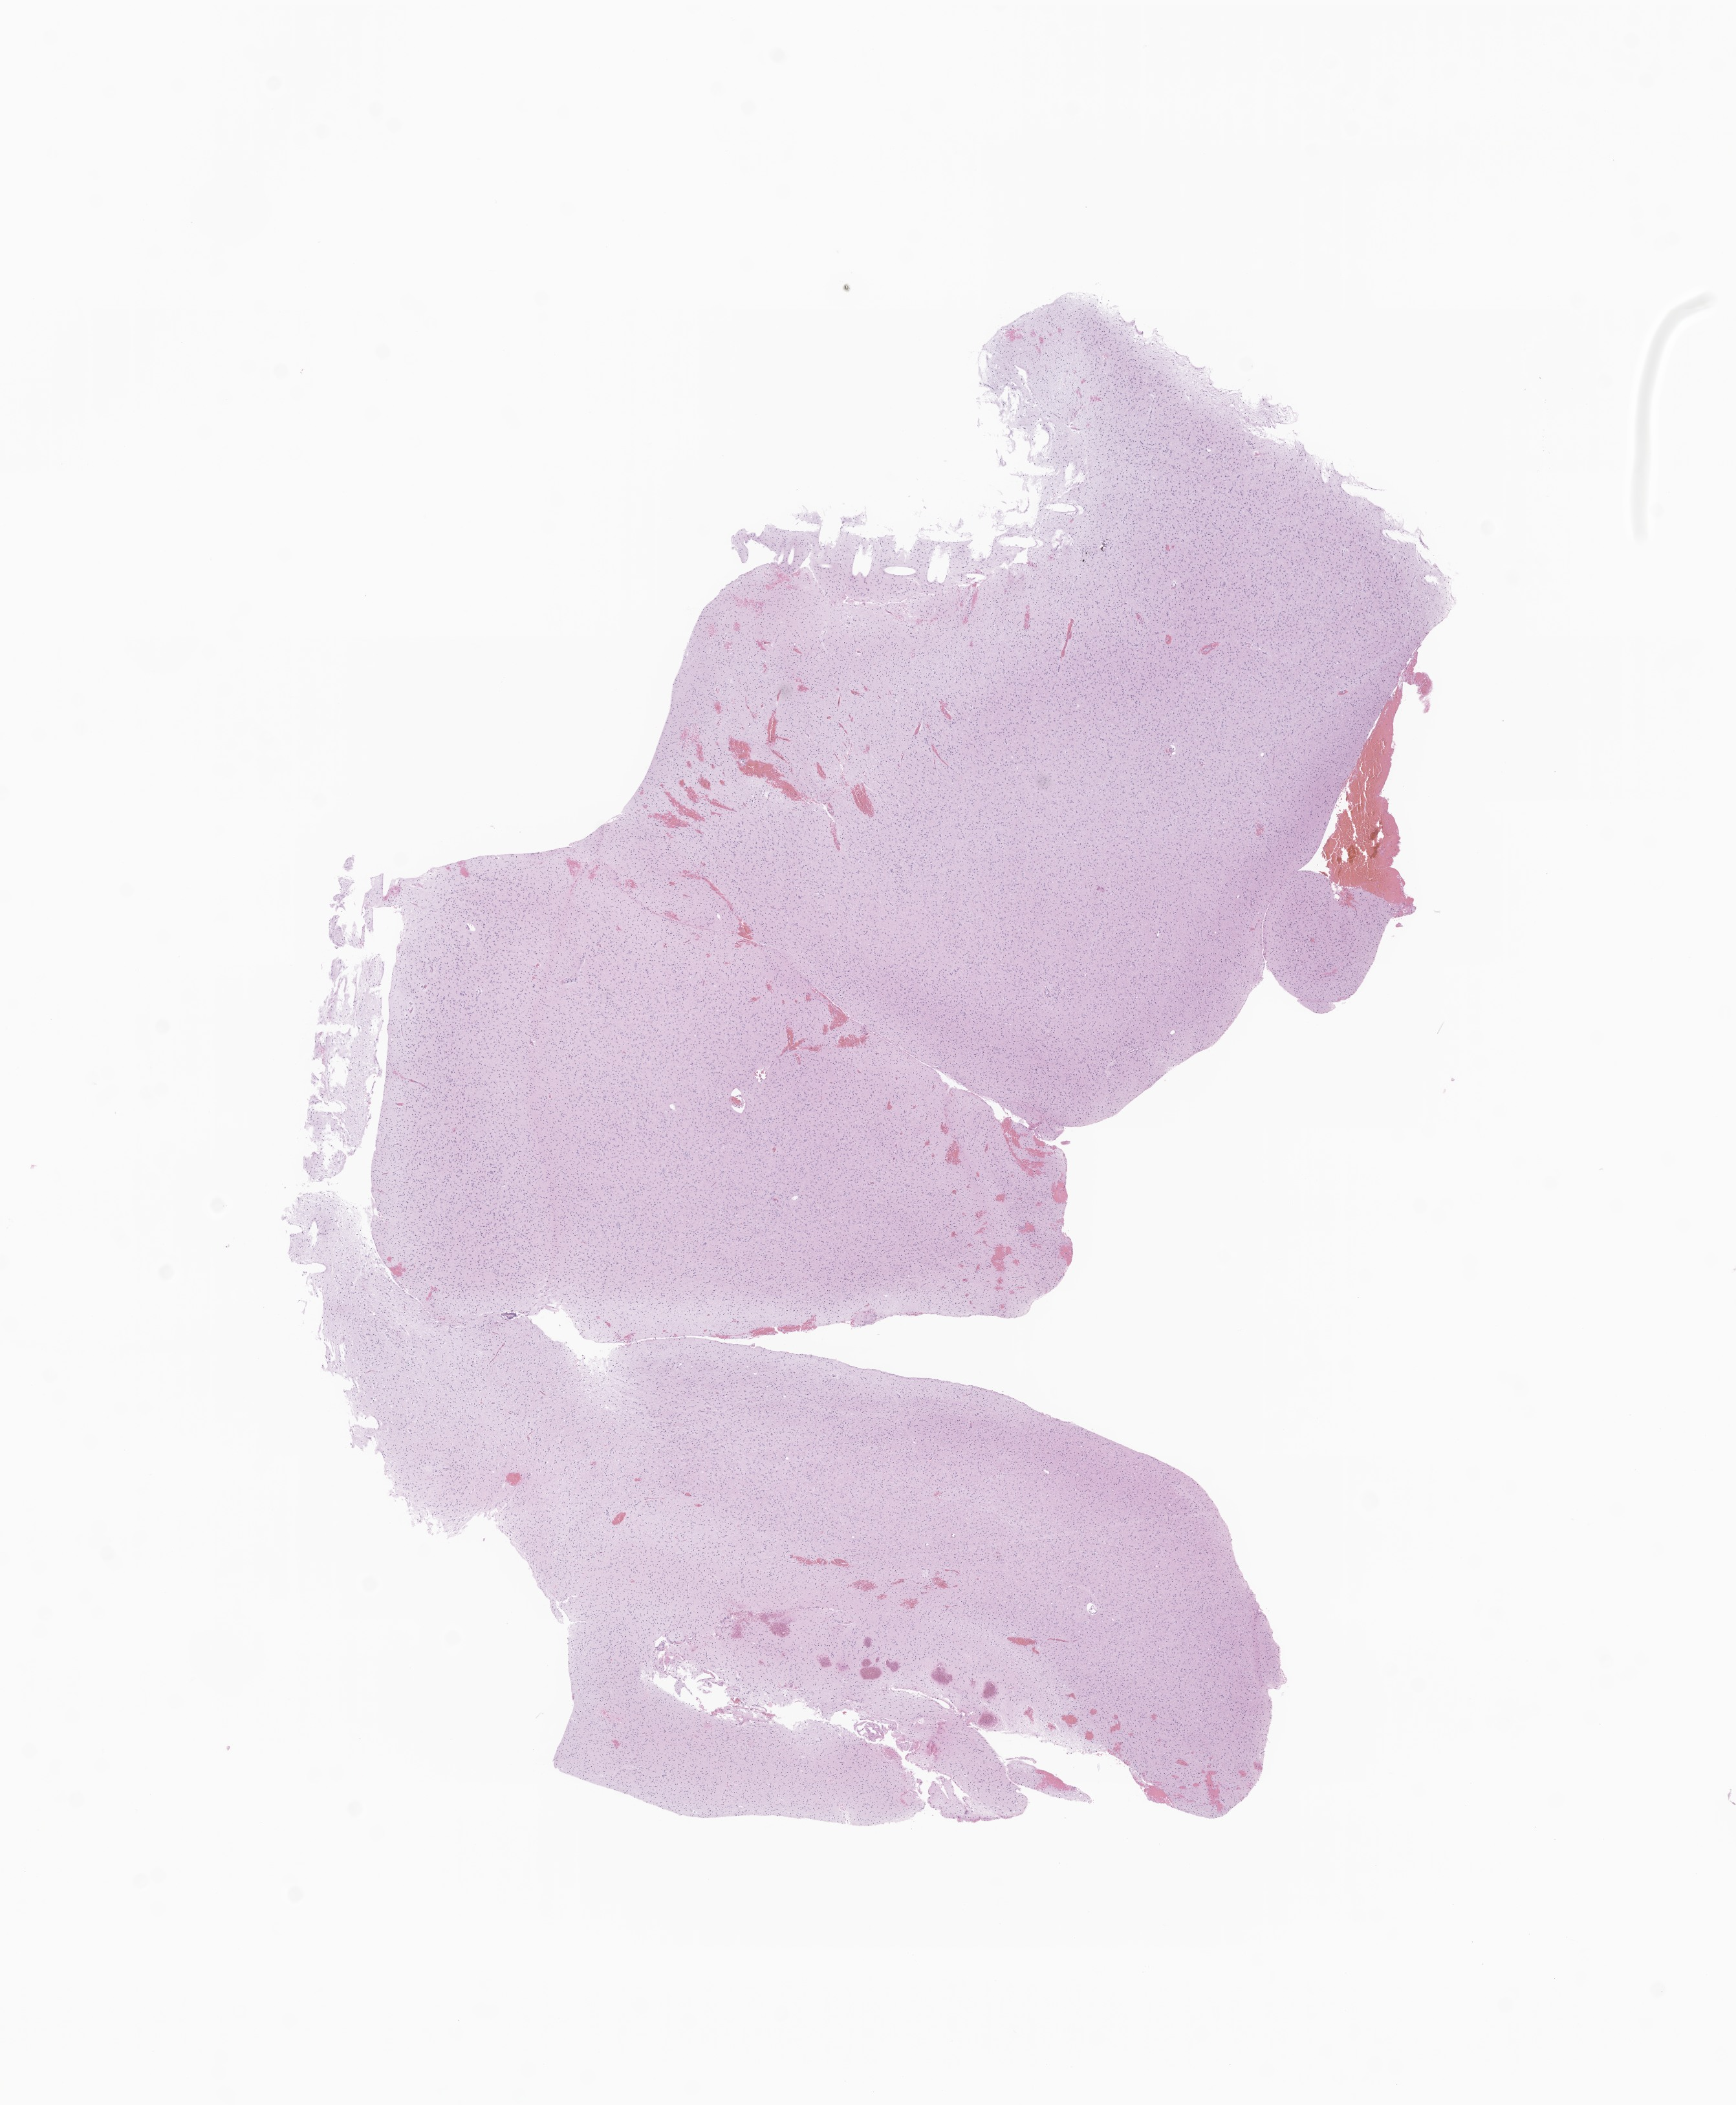
Digitized haematoxylin and eosin-stained section of tumor tissue from the brain — shown as a low-resolution overview of the whole scanned area (about 11.3 x 13.7 mm); formalin-fixed paraffin-embedded section. Patient male; age 62 months (5 years 2 months).
Recorded diagnosis: Glioma, malignant.